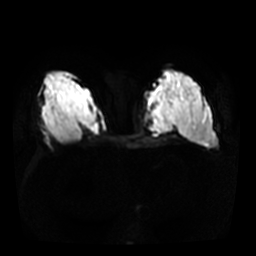
Breast MRI, one axial slice. Position 14 of 36 along the scan axis. Diffusion-weighted series; image 2 of 4 stored at this slice position (different b-values; order by instance number). 3 T. 5 mm slice thickness. 256 × 256 image matrix, field of view 340 × 340 mm. Female patient.
Structures marked on this image (manually delineated by an expert):
- tumour on diffusion-weighted imaging: bounding box <167,89,173,108> (left, top, right, bottom; pixels)